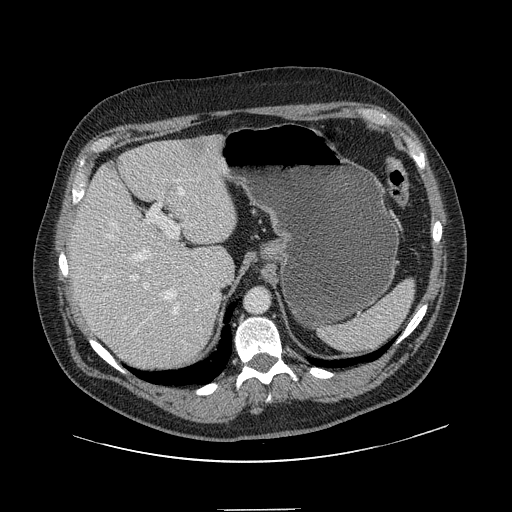
Contrast-enhanced abdominal CT, one axial slice; position 107 of 154 along the scan axis; 120 kVp; intravenous contrast given; soft-tissue window (W 400 / L 40 HU); 2.5 mm slice thickness; 512 × 512 image matrix. Male patient, age 61 years. Case-level facts recorded for this patient, not image findings: diagnosis: colorectal cancer liver metastases, imaged before liver resection; multiple liver metastases: yes; largest metastasis: 2.6 cm; disease in both lobes: yes.
Structures marked on this image (outlined manually by an expert reader):
- hepatic veins: bounding box (x1, y1, x2, y2) in pixels: (106, 187, 184, 315)
- liver: (69, 137, 237, 372)
- planned liver remnant (the part of the liver to remain after resection): (69, 144, 238, 359)
- portal vein (with intrahepatic branches): (124, 180, 185, 319)
- liver metastasis: (189, 141, 205, 159)